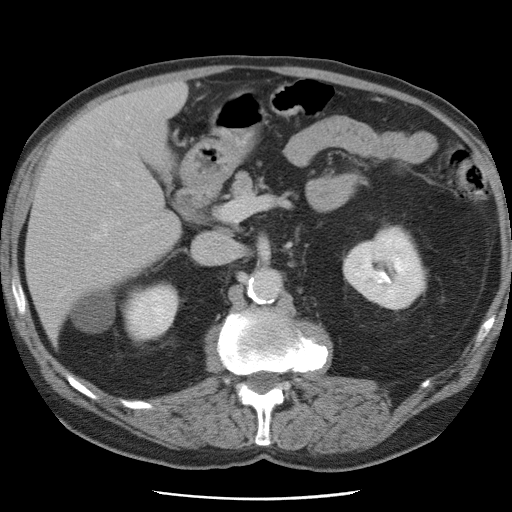
Contrast-enhanced abdominal CT, one axial slice; slice 38 of 78 in the series (ordered by position); 120 kVp; intravenous contrast given; soft-tissue window (W 400 / L 40 HU); 5 mm slice thickness; 512 × 512 image matrix, field of view 337 × 337 mm. Male patient, age 75 years. From the clinical record (not read from this slice): diagnosis: colorectal cancer liver metastases, imaged before liver resection; multiple liver metastases: yes; largest metastasis: 2.4 cm.
Structures marked on this image (manually delineated by an expert):
- hepatic veins: bounding box [x1, y1, x2, y2] px = [90, 118, 128, 242]
- liver: [27, 84, 186, 337]
- planned liver remnant (the part of the liver to remain after resection): [27, 118, 180, 338]
- portal vein (with intrahepatic branches): [114, 183, 118, 186]